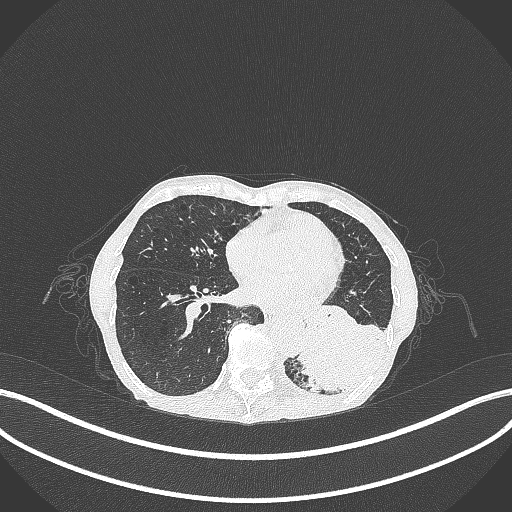
Chest CT, one axial slice. Position 99 of 347 along the scan axis. Reconstruction kernel B70f. 120 kVp. Lung window (W 1500 / L -600 HU). 1 mm slice thickness. 512 × 512 image matrix, field of view 400 × 400 mm. Female patient, age 70 years. Case-level facts recorded for this patient, not image findings: clinical TNM (as recorded): T3 N0 M0; histopathological grade: G3.
Annotated regions visible in this slice (rectangle marked by the reading radiologist):
- lung tumour (recorded histology: small cell carcinoma): bounding box (x1, y1, x2, y2) in pixels: (293, 318, 397, 403)